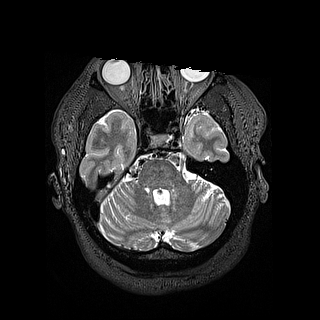
Brain MRI from a brain-tumour surgery series, one axial slice. Slice 109 of 144 in the series (ordered by position). 1.2 mm slice thickness. 320 × 320 image matrix, field of view 254 × 254 mm. From the clinical record (not read from this slice): histopathology: Astrocytoma; WHO grade: 2; IDH mutation: yes.
Annotated regions visible in this slice (expert manual segmentation):
- tumour: bounding box [x1, y1, x2, y2] px = [189, 131, 194, 138]